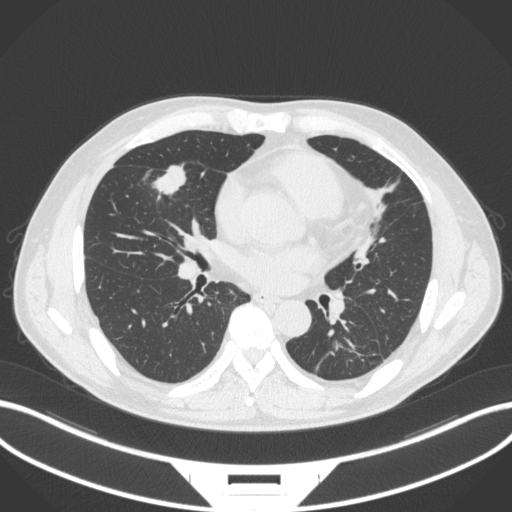
Chest CT, one axial slice; position 146 of 399 along the scan axis; reconstruction kernel B31f; 120 kVp; lung window (W 1500 / L -600 HU); 1 mm slice thickness; 512 × 512 image matrix, field of view 400 × 400 mm. Patient: male, 59 years. From the clinical record (not read from this slice): clinical TNM (as recorded): T2a N1 M0.
Structures marked on this image (rectangle marked by the reading radiologist):
- lung tumour (recorded histology: adenocarcinoma): box from (x=151, y=162) to (x=190, y=200) px